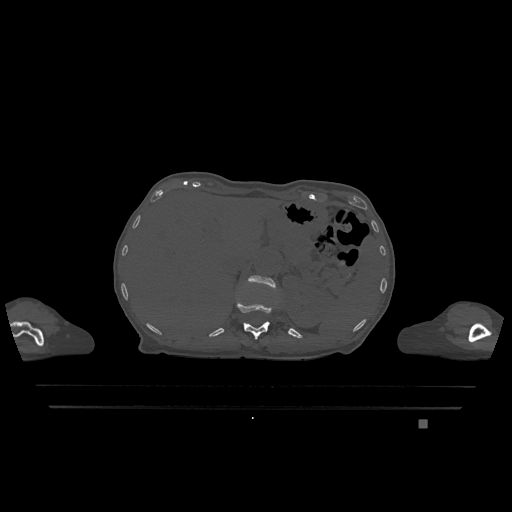
CT including the spine, one axial slice; slice 522 of 1317 in the series (ordered by position); bone window (W 1800 / L 400 HU); 0.5 mm slice thickness; 512 × 512 image matrix, field of view 500 × 500 mm. Female patient, age 74 years. Case-level facts recorded for this patient, not image findings: primary cancer: lung.
Annotated regions visible in this slice (semi-automatic segmentation, software-assisted and operator-edited):
- L1 vertebra: bounding box [x1, y1, x2, y2] px = [248, 275, 276, 289]
- T12 vertebra: [236, 298, 273, 340]